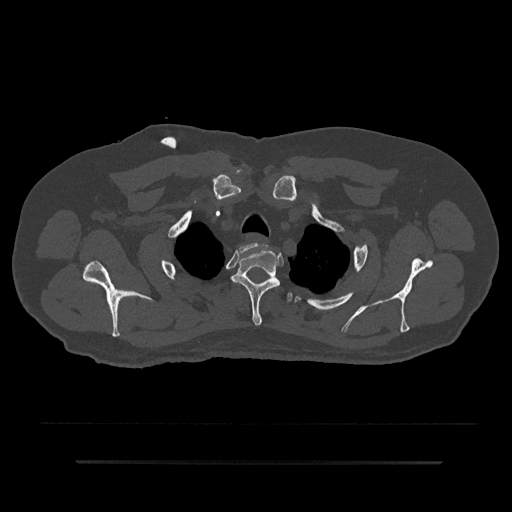
CT including the spine, one axial slice; reconstruction kernel Br40s/3; 120 kVp; bone window (W 1800 / L 400 HU); 0.5 mm slice thickness; 512 × 512 image matrix. Patient: male, 59 years. From the clinical record (not read from this slice): primary cancer: bile ducts; vertebrae with lytic lesions (as recorded): T10.
Structures marked on this image (semi-automatically segmented with operator editing):
- T1 vertebra: box from (x=239, y=244) to (x=256, y=253) px
- T2 vertebra: (x=231, y=250)–(x=280, y=326)
- T3 vertebra: (x=287, y=292)–(x=292, y=303)